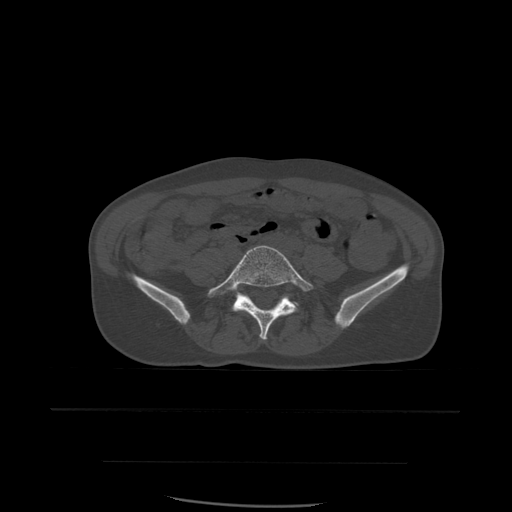
CT including the spine, one axial slice; slice 147 of 574 in the series (ordered by position); bone window (W 1800 / L 400 HU); 1.25 mm slice thickness; 512 × 512 image matrix, field of view 392 × 392 mm. Patient age 48 years. Case-level facts recorded for this patient, not image findings: primary cancer: lung; vertebrae with lytic lesions (as recorded): T11.
Annotated regions visible in this slice (semi-automatic segmentation, software-assisted and operator-edited):
- L5 vertebra: box from (x=208, y=246) to (x=317, y=340) px